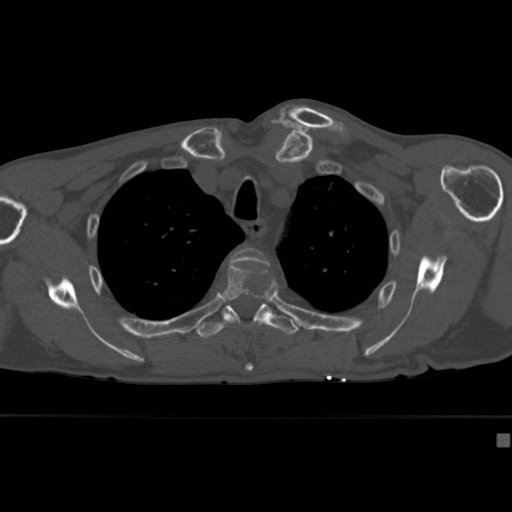
CT including the spine, one axial slice. Slice 318 of 430 in the series (ordered by position). Reconstruction kernel Br40s. Bone window (W 1800 / L 400 HU). 1.5 mm slice thickness. 512 × 512 image matrix, field of view 337 × 337 mm. Male patient, age 64 years. Case-level facts recorded for this patient, not image findings: primary cancer: uterus; vertebrae with lytic lesions (as recorded): T1, T4, T5, T7, L5.
Annotated regions visible in this slice (semi-automatically segmented with operator editing):
- T3 vertebra: bounding box (x1, y1, x2, y2) in pixels: (230, 247, 270, 267)
- T4 vertebra: (216, 262, 290, 372)
- T5 vertebra: (196, 303, 299, 339)